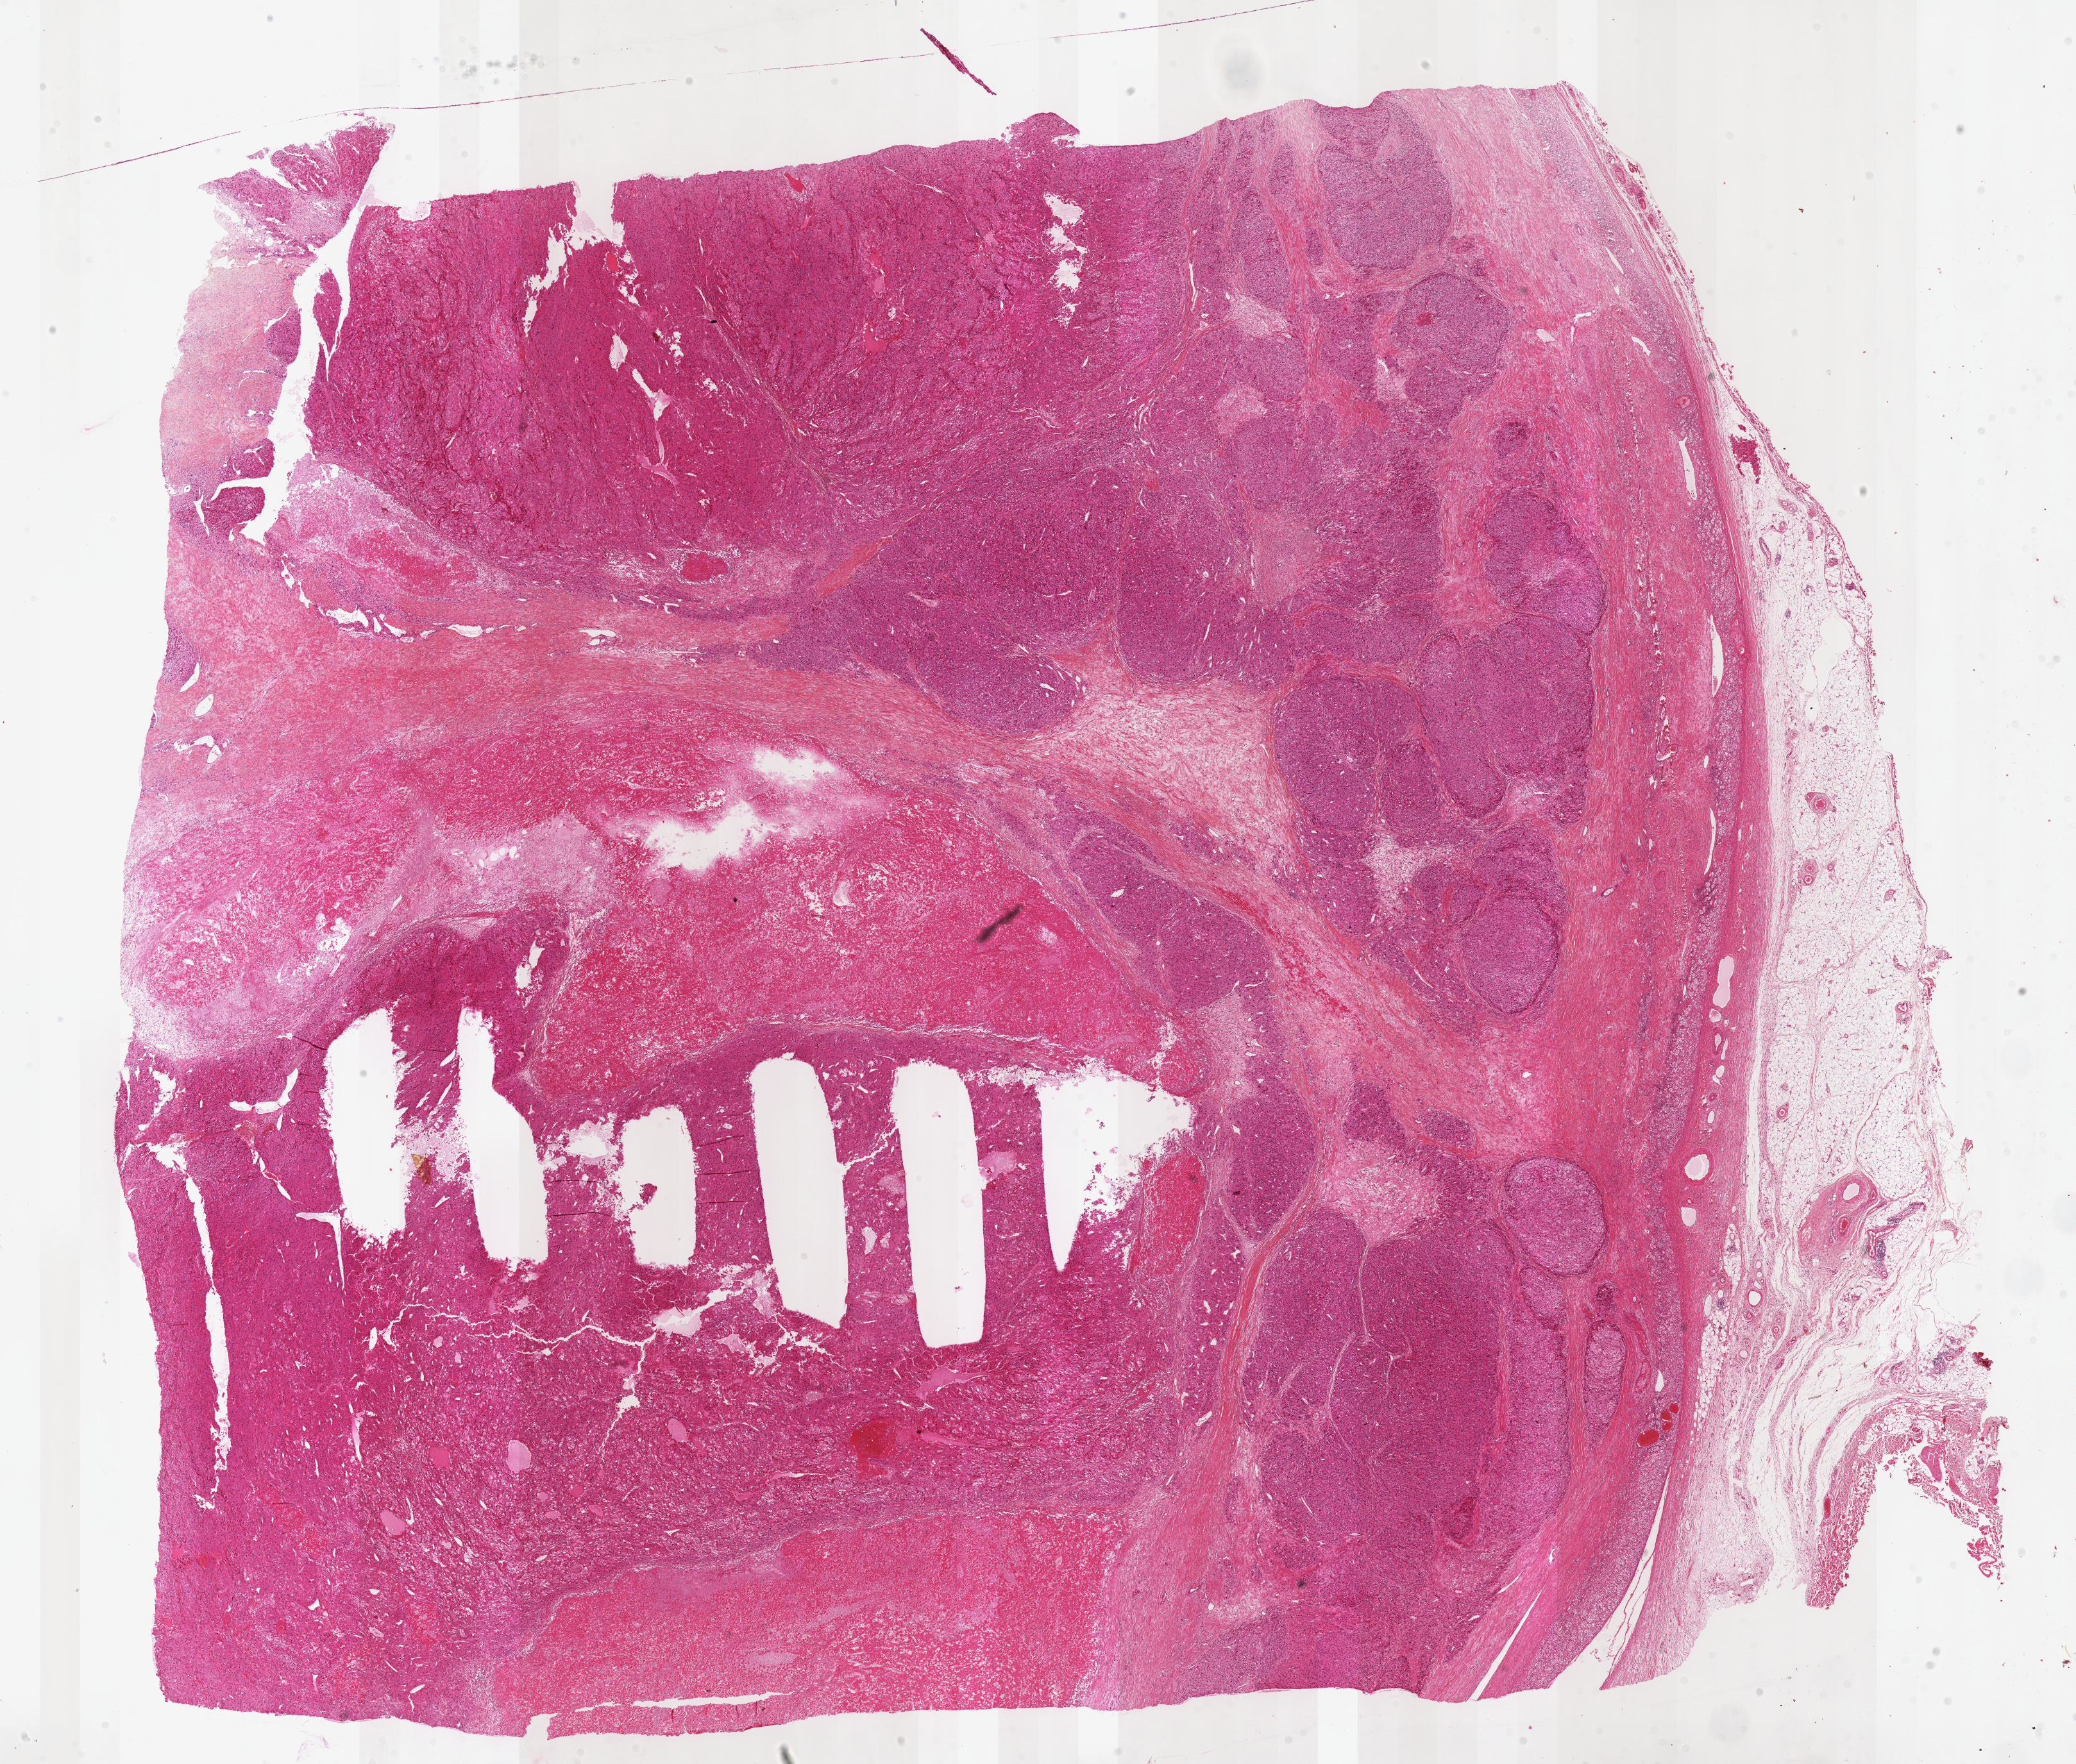
Digitized H&E-stained tissue section (whole slide) — shown as a low-resolution overview of the whole scanned area (about 26.2 x 22.2 mm); FFPE section; adrenal cortex, primary tumour sample. Male patient; age at initial diagnosis 23 years.
- lymph nodes positive (case pathology): 0 of 32 examined
- pathologic diagnosis: Adrenal cortical carcinoma (cortex of adrenal gland)